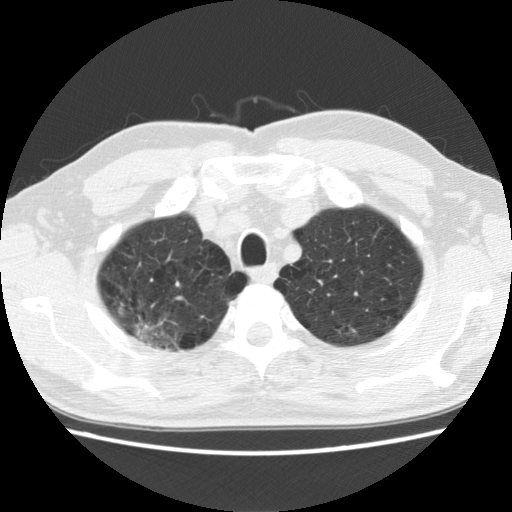
Low-dose screening chest CT, axial slice; baseline screening round; lung window (W 1500 / L -600 HU); standard (soft-tissue) reconstruction kernel (STANDARD); 120 kVp; slice 24 of 142 in the series. Male participant, aged 64 years at enrolment. Former smoker at enrolment.
Expert-annotated lung lesion, bounding box [x1, y1, x2, y2] px = [107, 288, 195, 362]. The exam's reader record, not a measurement of the box and not confirmed to be the same lesion: non-calcified nodule or mass ≥4 mm, right upper lobe, 39 × 31 mm, spiculated (stellate) margins, mixed attenuation. Lung cancer was diagnosed 74 days after this screen: adenocarcinoma, NOS, right upper lobe, moderately differentiated (G2), stage IB (AJCC 6th edition), 40 mm at pathology.